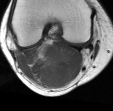
MRI of an extremity soft-tissue mass, one axial slice; MR volume resampled by the dataset authors to the PET/CT grid (not the native acquisition matrix); 3.27 mm slice thickness; 113 × 111 image matrix, field of view 110 × 108 mm. Female patient. From the clinical record (not read from this slice): histological type: liposarcoma; site of the primary tumour: right thigh.
Outlined on this slice (expert contour drawn on MRI and transferred to this co-registered scan by the dataset authors):
- gross tumour volume (mass): bounding box [x1, y1, x2, y2] px = [28, 42, 77, 88]